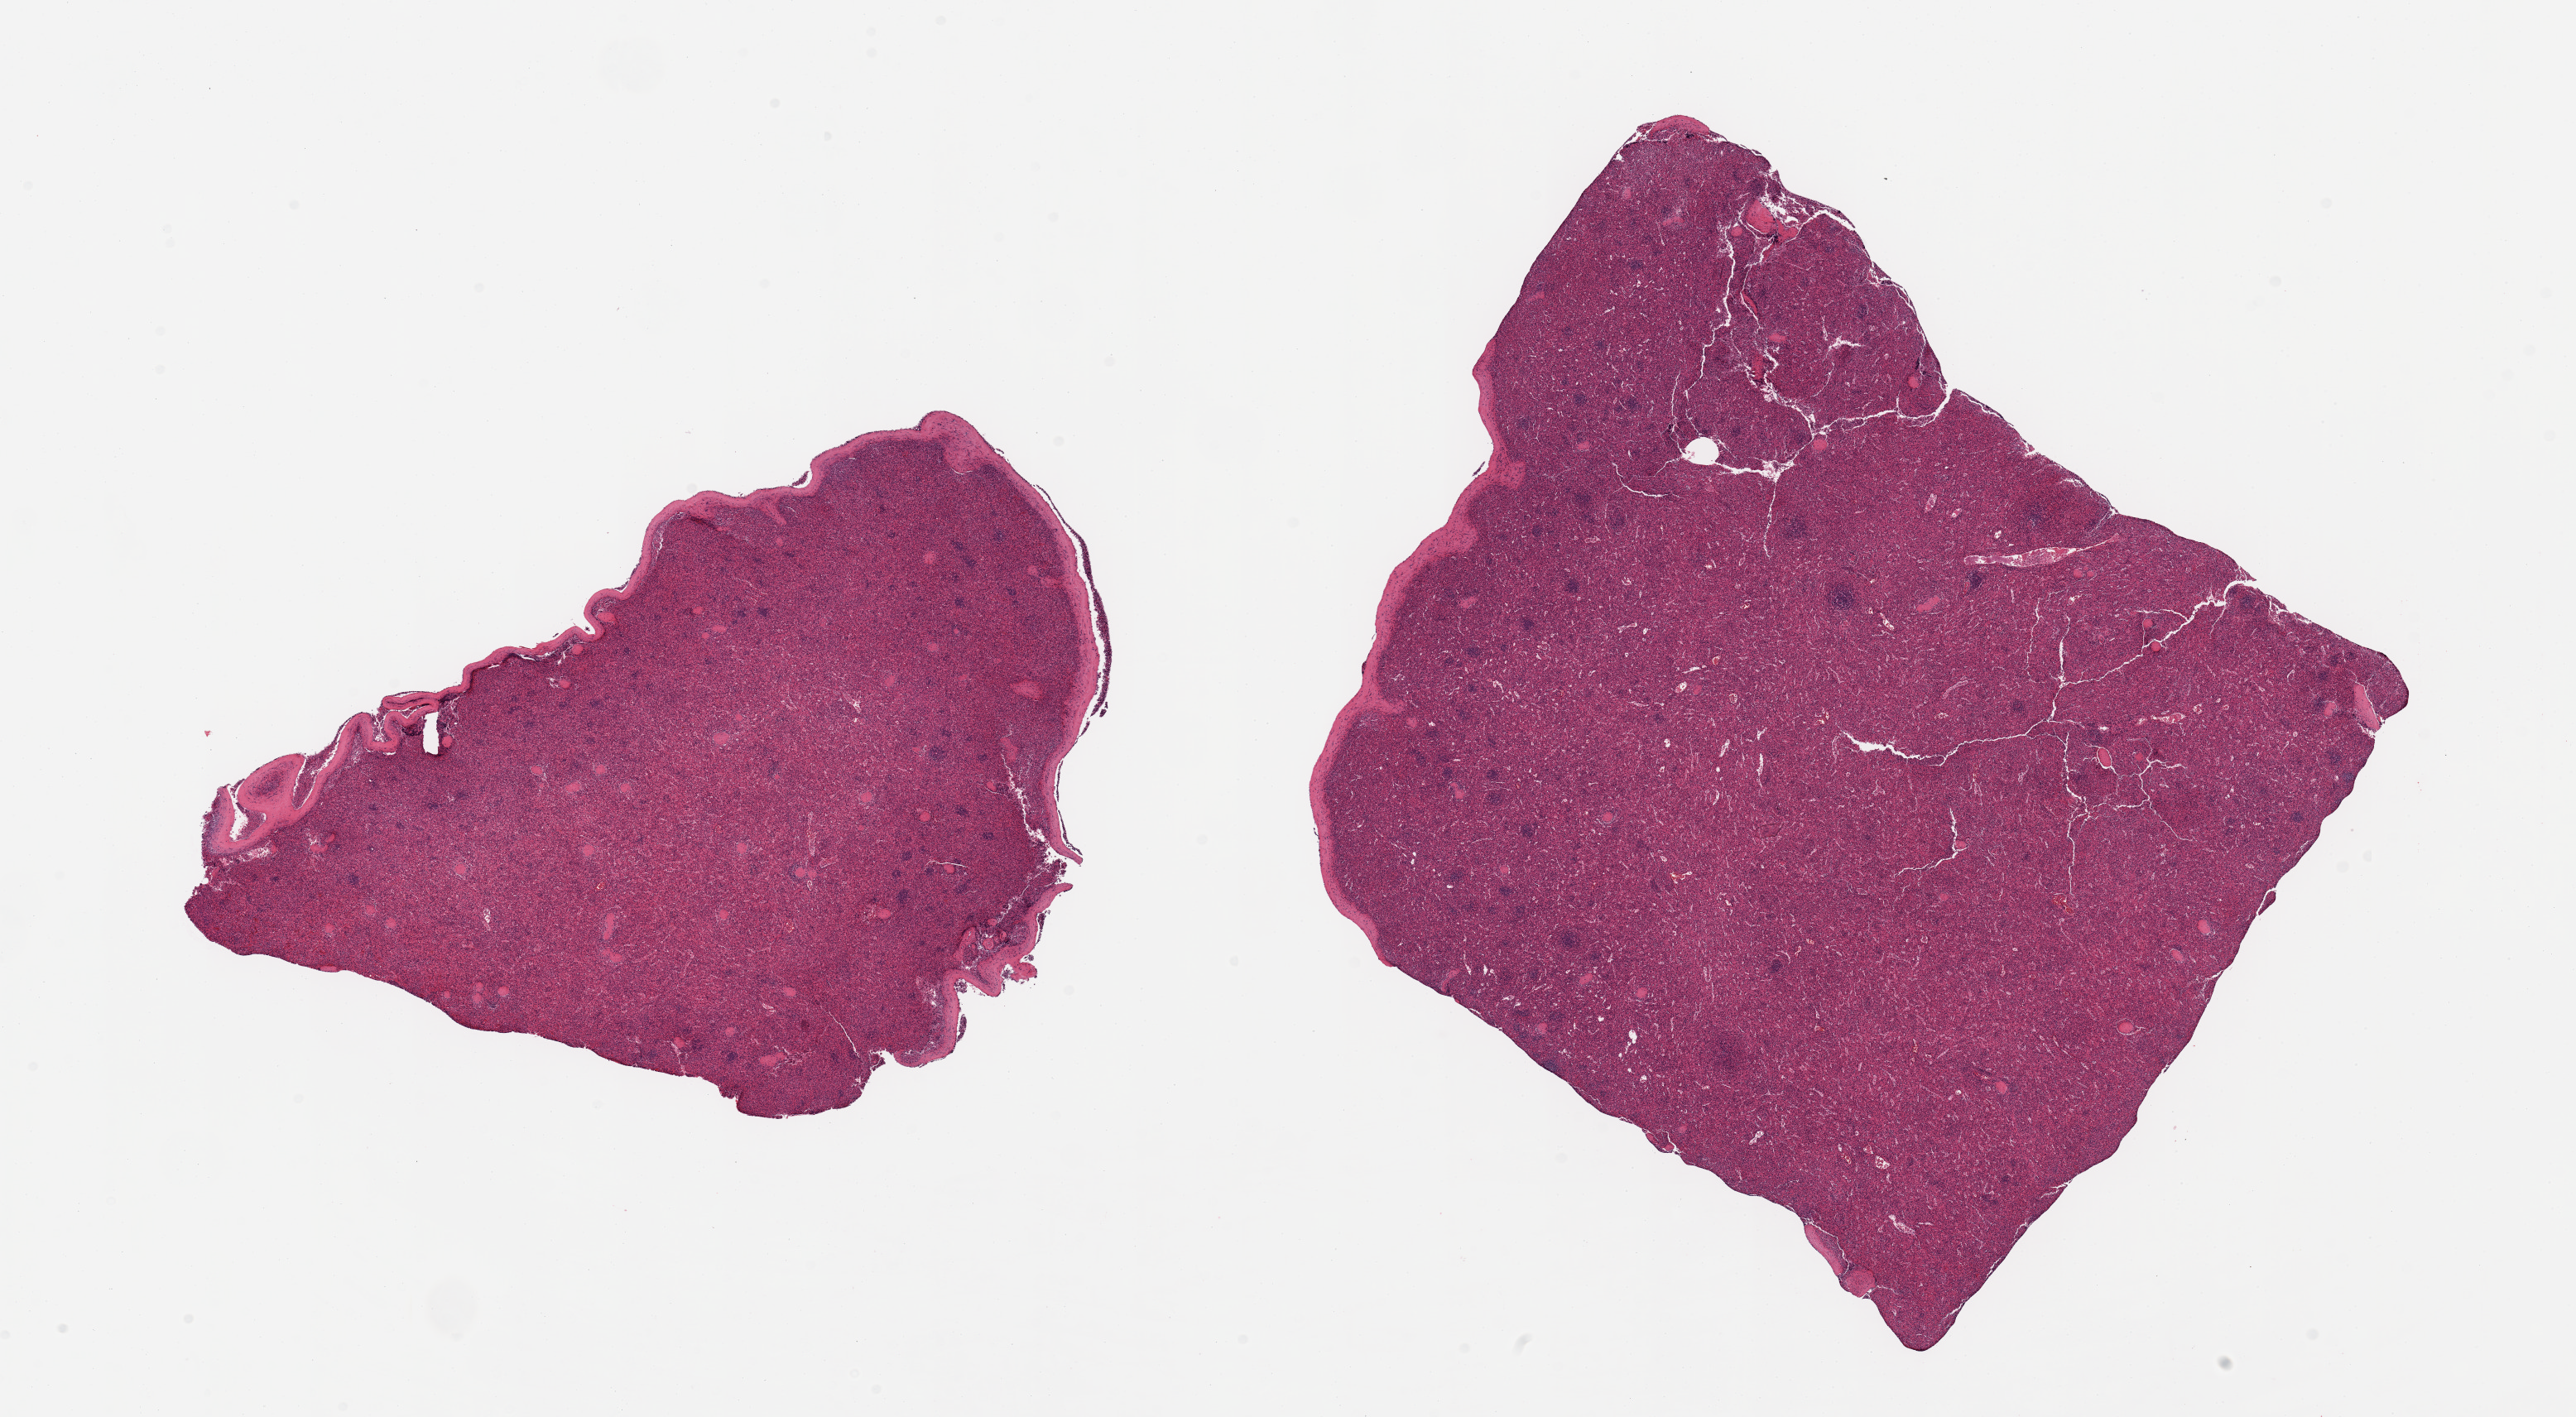
Whole-slide image, hematoxylin and eosin (H&E) stain — shown as a low-resolution overview of the whole scanned area (about 24.6 x 13.5 mm, acquisition: 20x scan). PAXgene-fixed, paraffin-embedded tissue. Sampled site (target tissue): spleen. Donor tissue sample. Donor sex: female.
Review note (as recorded): 2 pieces, no abnormalities.